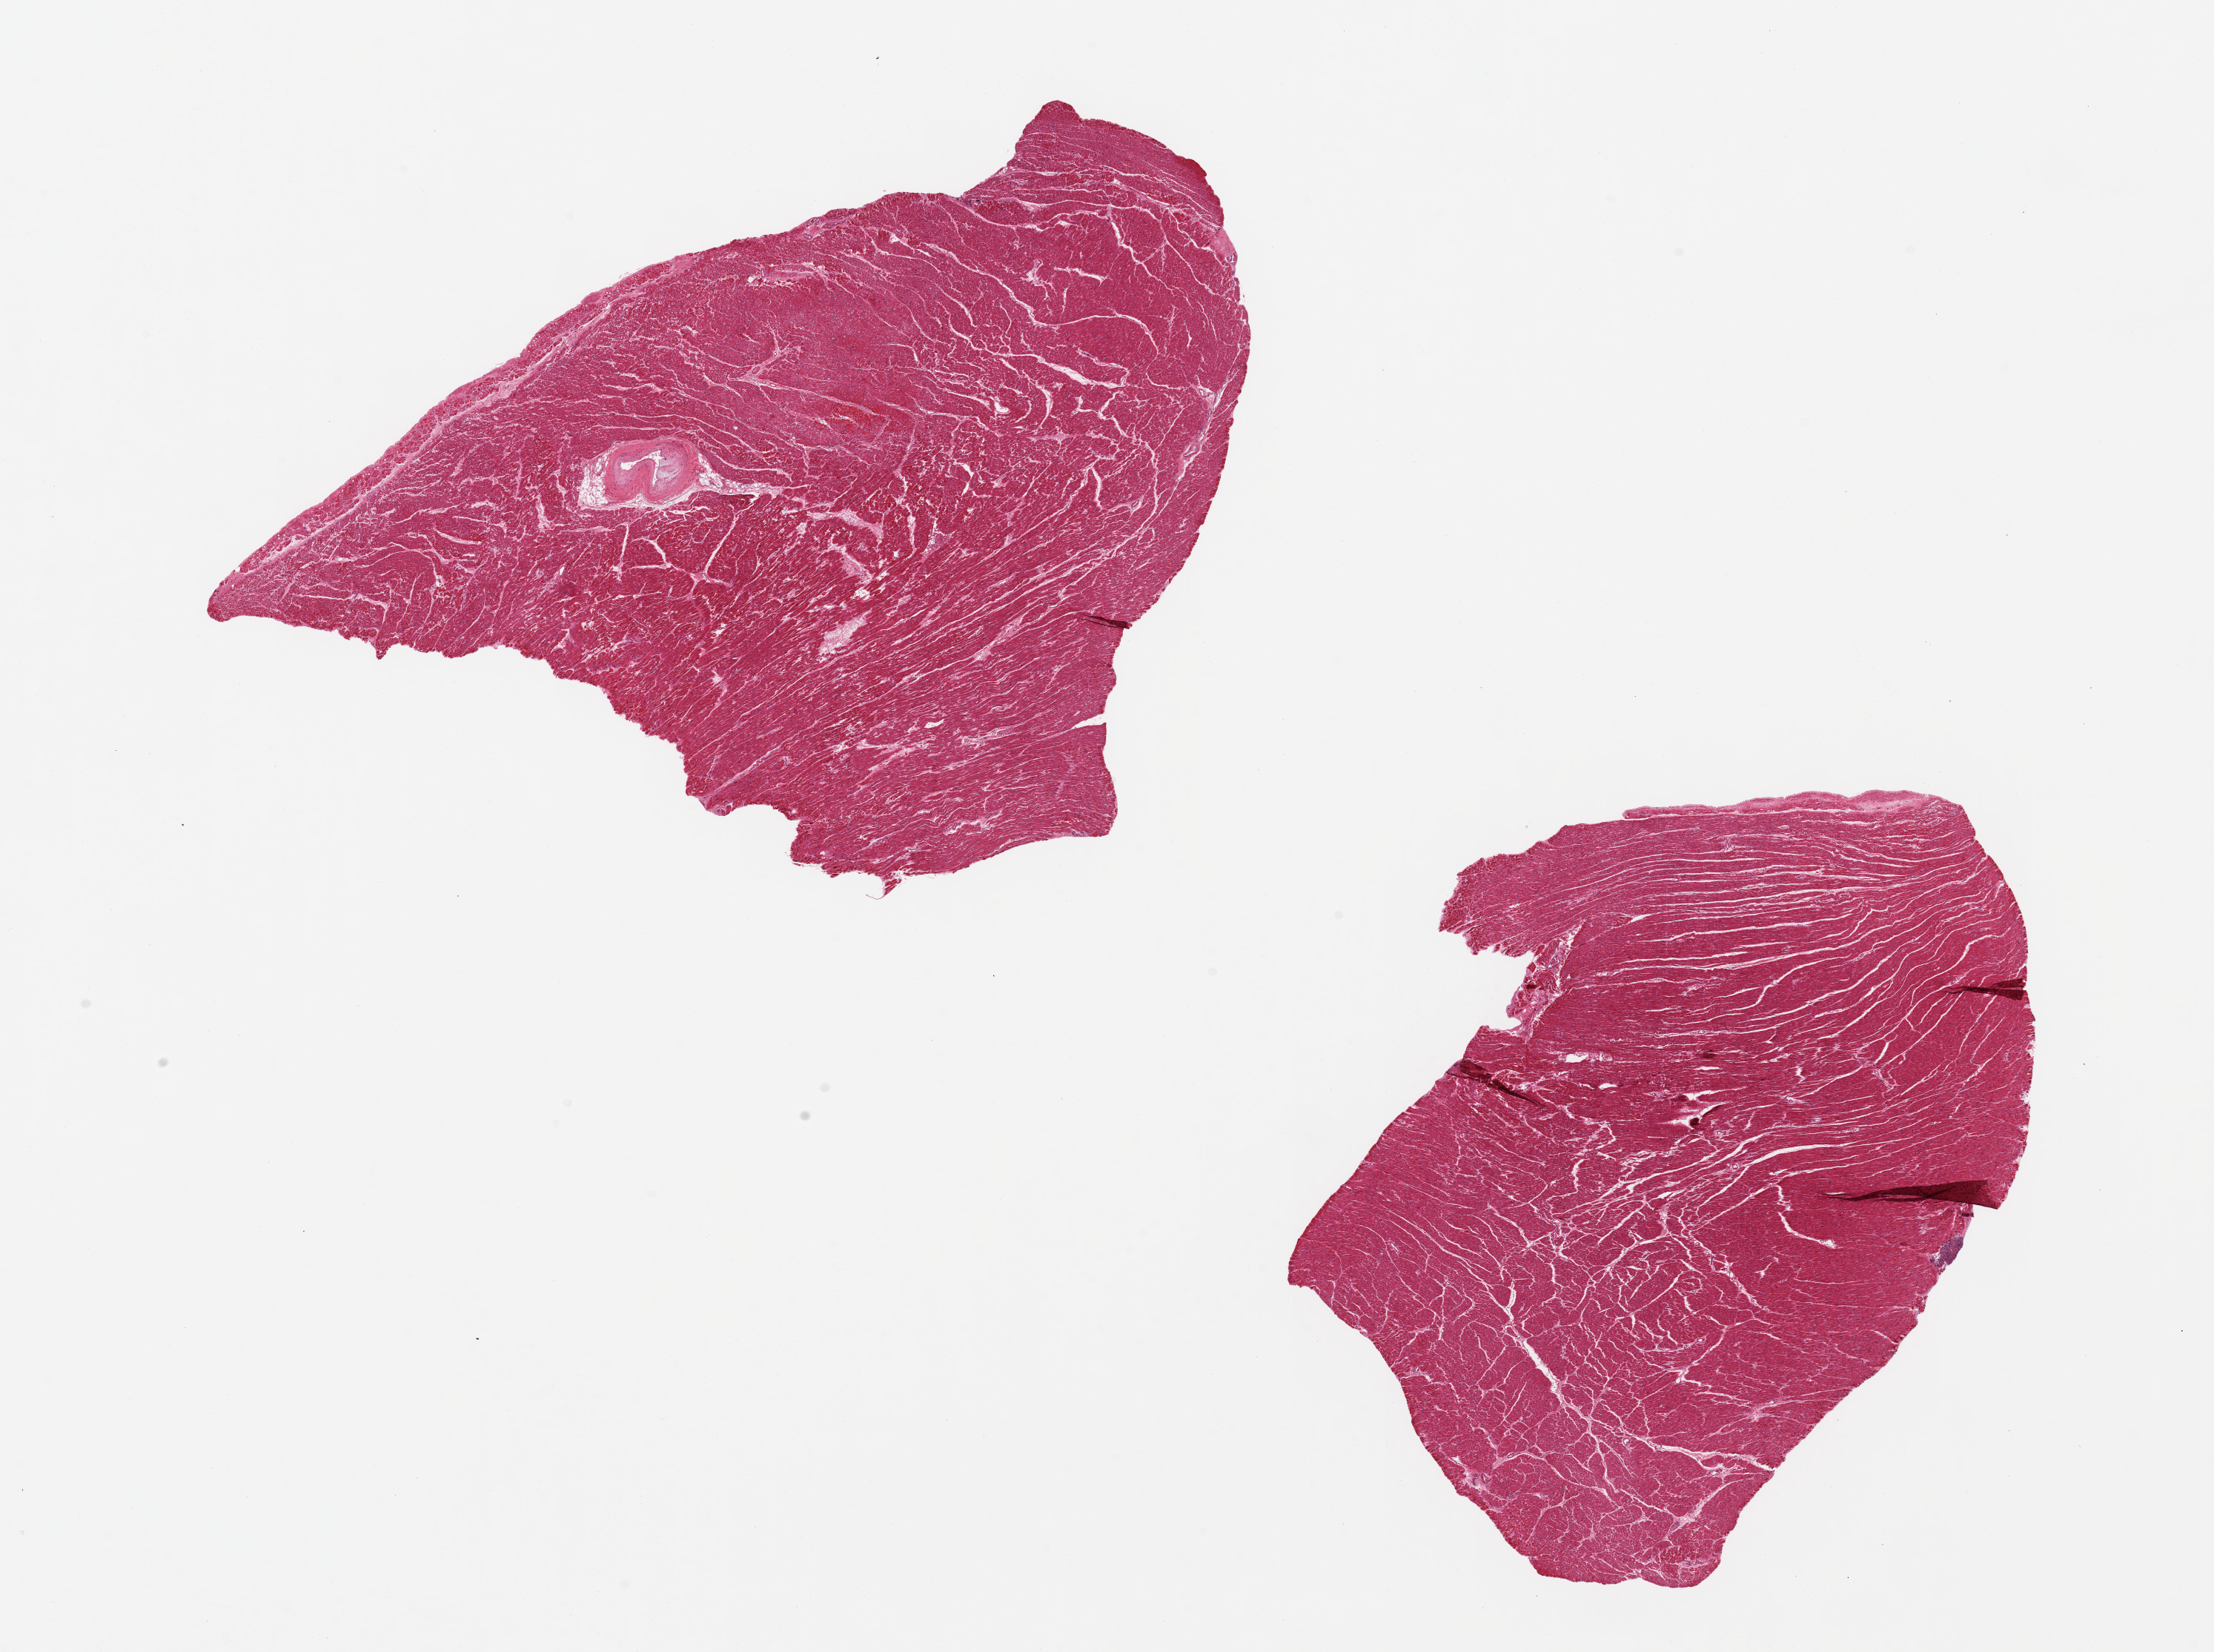
Haematoxylin and eosin whole-slide image, low-resolution overview of the scanned area, about 23.6 x 17.6 mm; PAXgene-fixed, paraffin-embedded tissue; target tissue: heart; tissue donor sample. Donor: female.
• pathologist's review note for this sample: 2 pieces 11x7 & 9x5 mm; no extraneous tissue